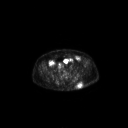
FDG PET of an extremity soft-tissue mass (from a PET/CT study), one axial slice; slice 75 of 267 in the series (ordered by position); 128 × 128 image matrix. Patient: male, 69 years. Case-level facts recorded for this patient, not image findings: histological type: leiomyosarcoma; grade: intermediate; site of the primary tumour: left pelvis.
Outlined on this slice (expert contour drawn on MRI and transferred to this co-registered scan by the dataset authors):
- gross tumour volume (mass): bounding box <76,82,83,89> (left, top, right, bottom; pixels)